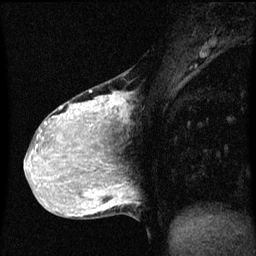
Breast MRI (dynamic contrast-enhanced), one sagittal slice; position 23 of 60 along the scan axis; dynamic contrast-enhanced series, image 2 of 3 at this slice position (ordered by acquisition); 1.5 T; TE 4.2 ms, TR 8 ms; 2 mm slice thickness; 256 × 256 image matrix, field of view 200 × 200 mm. Patient: female, 36 years.
Annotated regions visible in this slice (semi-automatically segmented with operator editing):
- analysis volume of interest (the breast-tissue region the enhancement analysis was run in; not a lesion): bounding box (x1, y1, x2, y2) in pixels: (33, 72, 129, 169)
- tumour enhancement mask (voxels above the 70 % enhancement threshold inside the analysis volume of interest): (33, 90, 121, 169)